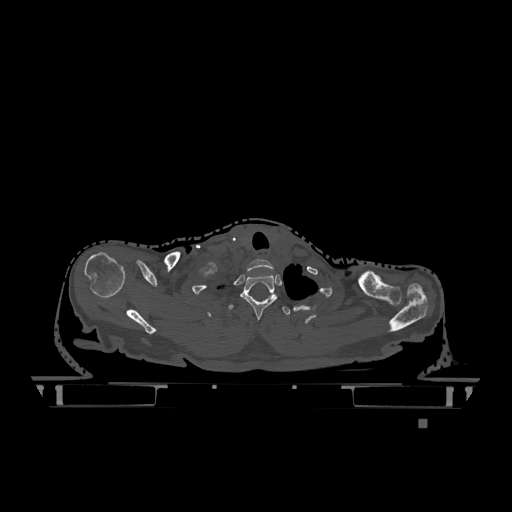
CT including the spine, one axial slice. Slice 994 of 1317 in the series (ordered by position). Bone window (W 1800 / L 400 HU). 0.5 mm slice thickness. 512 × 512 image matrix, field of view 500 × 500 mm. Patient: female, 74 years. Case-level facts recorded for this patient, not image findings: primary cancer: lung; vertebrae with lytic lesions (as recorded): T1, T4, T5, T6, L4, L5.
Annotated regions visible in this slice (semi-automatic segmentation, software-assisted and operator-edited):
- T1 vertebra: bounding box <240,274,278,320> (left, top, right, bottom; pixels)
- T2 vertebra: <228,295,291,315>